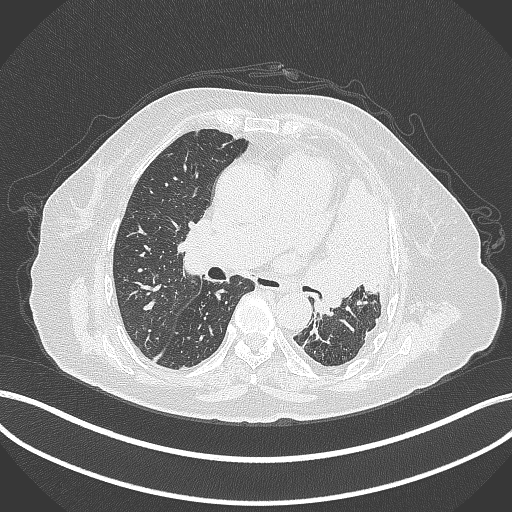
Chest CT, one axial slice. Slice 209 of 399 in the series (ordered by position). Reconstruction kernel B70f. 120 kVp. Lung window (W 1500 / L -600 HU). 1 mm slice thickness. 512 × 512 image matrix, field of view 400 × 400 mm. Female patient, age 75 years. Case-level facts recorded for this patient, not image findings: clinical TNM (as recorded): T3 N3 M1.
Outlined on this slice (bounding box drawn by a radiologist):
- lung tumour (recorded histology: adenocarcinoma): bounding box [x1, y1, x2, y2] px = [305, 171, 390, 322]